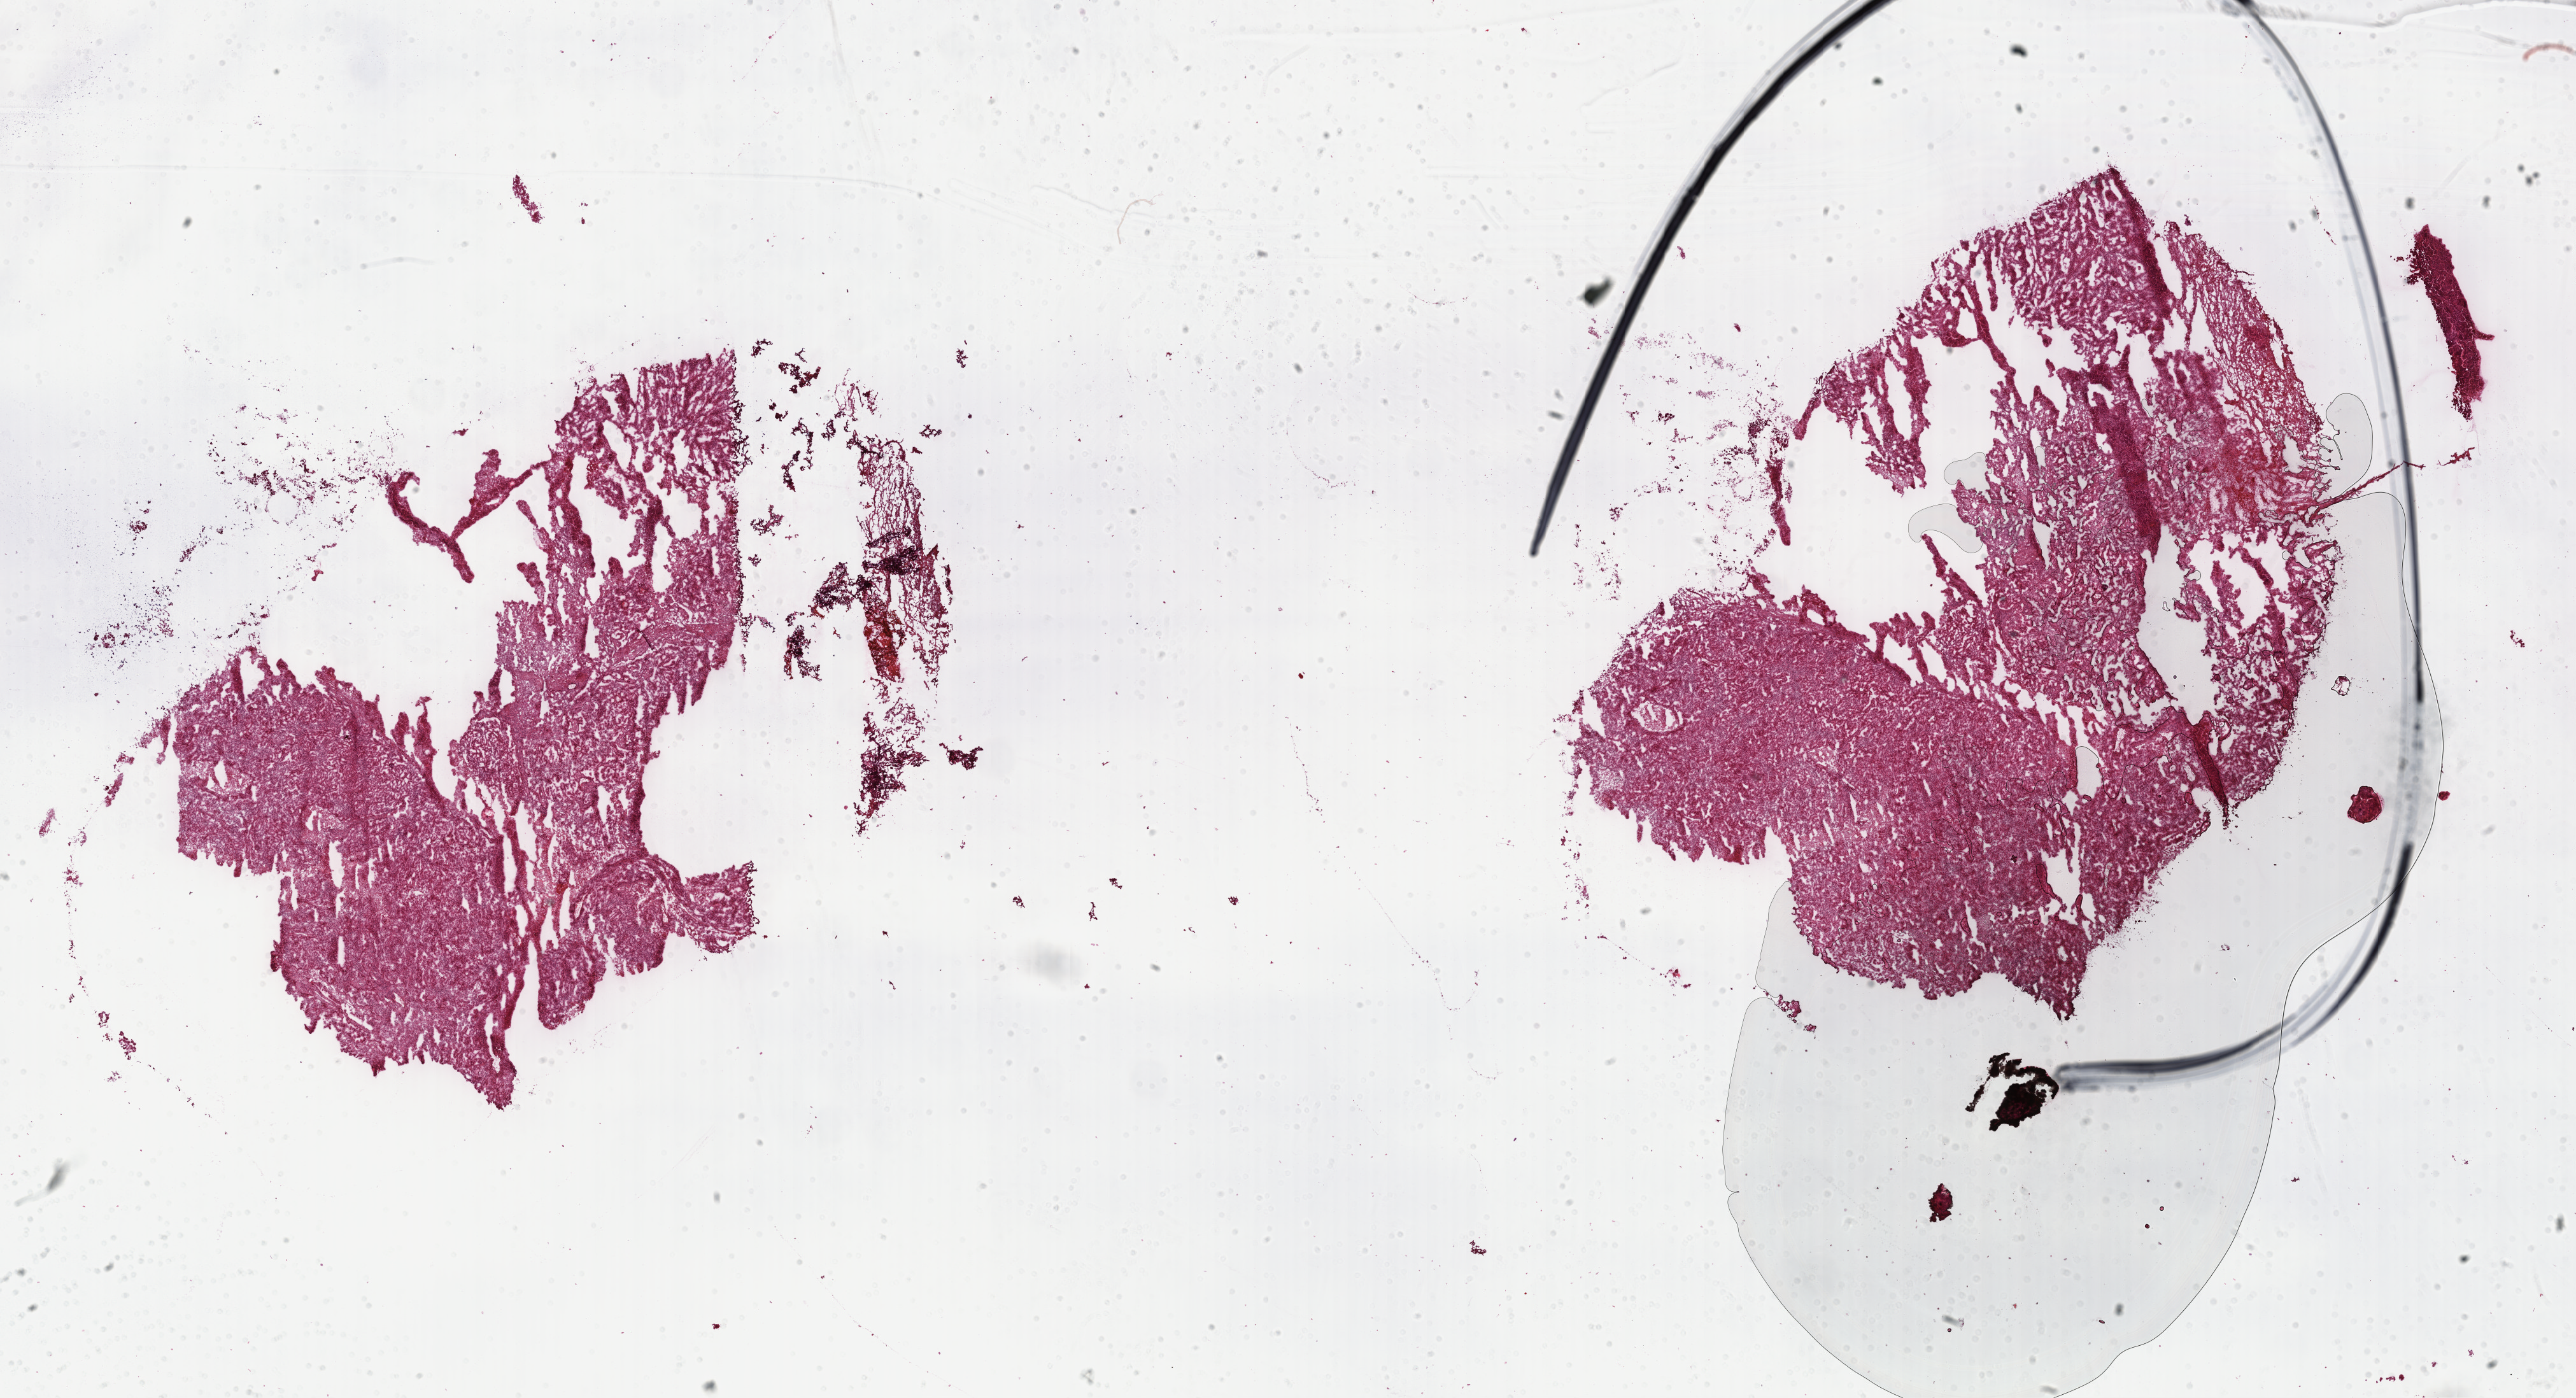
Digitized H&E tissue section (whole slide), a low-resolution overview of the entire scanned area, about 32.7 x 17.8 mm, frozen section from the top of the tissue portion, primary tumour sample from the kidney. Male, age 54 years at initial diagnosis. Composition of this section per pathologist review: tumour cells 100%, tumour nuclei 75%, normal cells 0%, stromal cells 0%, necrosis 0%. Infiltration values recorded for this section: lymphocyte infiltration 1%, monocyte infiltration 7%, neutrophil infiltration 0%.
Histologic diagnosis: Papillary adenocarcinoma, NOS. Laterality: left.